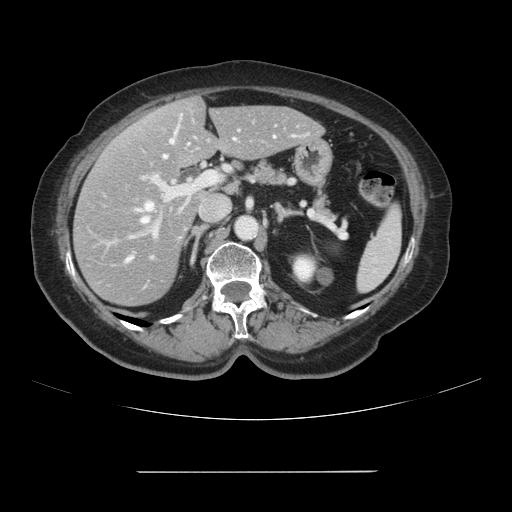
Contrast-enhanced abdominal CT, one axial slice. Slice 55 of 111 in the series (ordered by position). Intravenous contrast given. Soft-tissue window (W 400 / L 40 HU). 2.5 mm slice thickness. 512 × 512 image matrix. Female patient, age 74 years. From the clinical record (not read from this slice): diagnosis: colorectal cancer liver metastases, imaged before liver resection; multiple liver metastases: yes; largest metastasis: 1.1 cm; chemotherapy before resection: yes.
Annotated regions visible in this slice (outlined manually by an expert reader):
- hepatic veins: box from (x=127, y=139) to (x=174, y=261) px
- liver: (x=74, y=98)–(x=321, y=306)
- planned liver remnant (the part of the liver to remain after resection): (x=145, y=98)–(x=321, y=167)
- portal vein (with intrahepatic branches): (x=128, y=120)–(x=300, y=239)